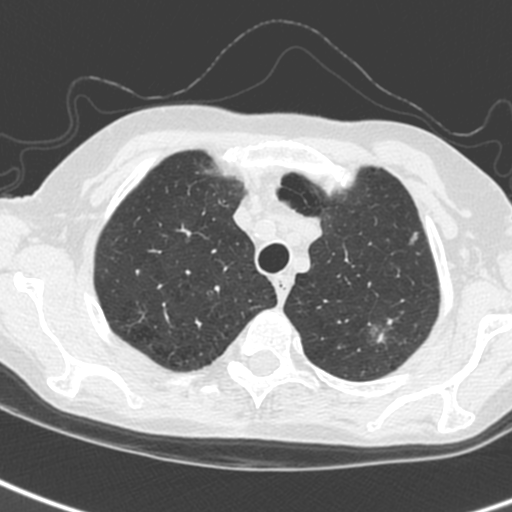
Chest CT (low-dose screening protocol), one axial image. Baseline annual screen. Lung window (W 1500 / L -600 HU). 1.3 mm slice thickness. Standard (soft-tissue) reconstruction kernel (C). Slice 32 of 242 in the series. Female participant, aged 61 years at enrolment. Current smoker at enrolment.
2 expert reader's lesion annotations on this slice (largest first), bounding box <356,310,413,354> (left, top, right, bottom; pixels); <394,223,432,258>. The screening reader recorded 2 non-calcified nodules or masses ≥4 mm on this exam (left upper lobe, left upper lobe); which of them these boxes mark is not recorded. Participant outcome: lung cancer diagnosed 29 days after this screen — small cell carcinoma, NOS, left upper lobe, stage IV (AJCC 6th edition).